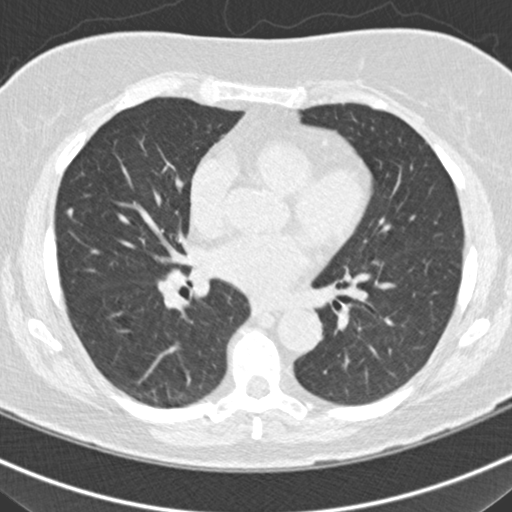
Low-dose screening chest CT, one axial slice. Slice 95 of 160 in the series (ordered by position). Reconstruction kernel B30f. 120 kVp. Lung window (W 1500 / L -600 HU). 512 × 512 image matrix.
Structures marked on this image (expert manual segmentation):
- lesion 1 (tumor, middle lobe of right lung): bounding box <68,209,73,216> (left, top, right, bottom; pixels)